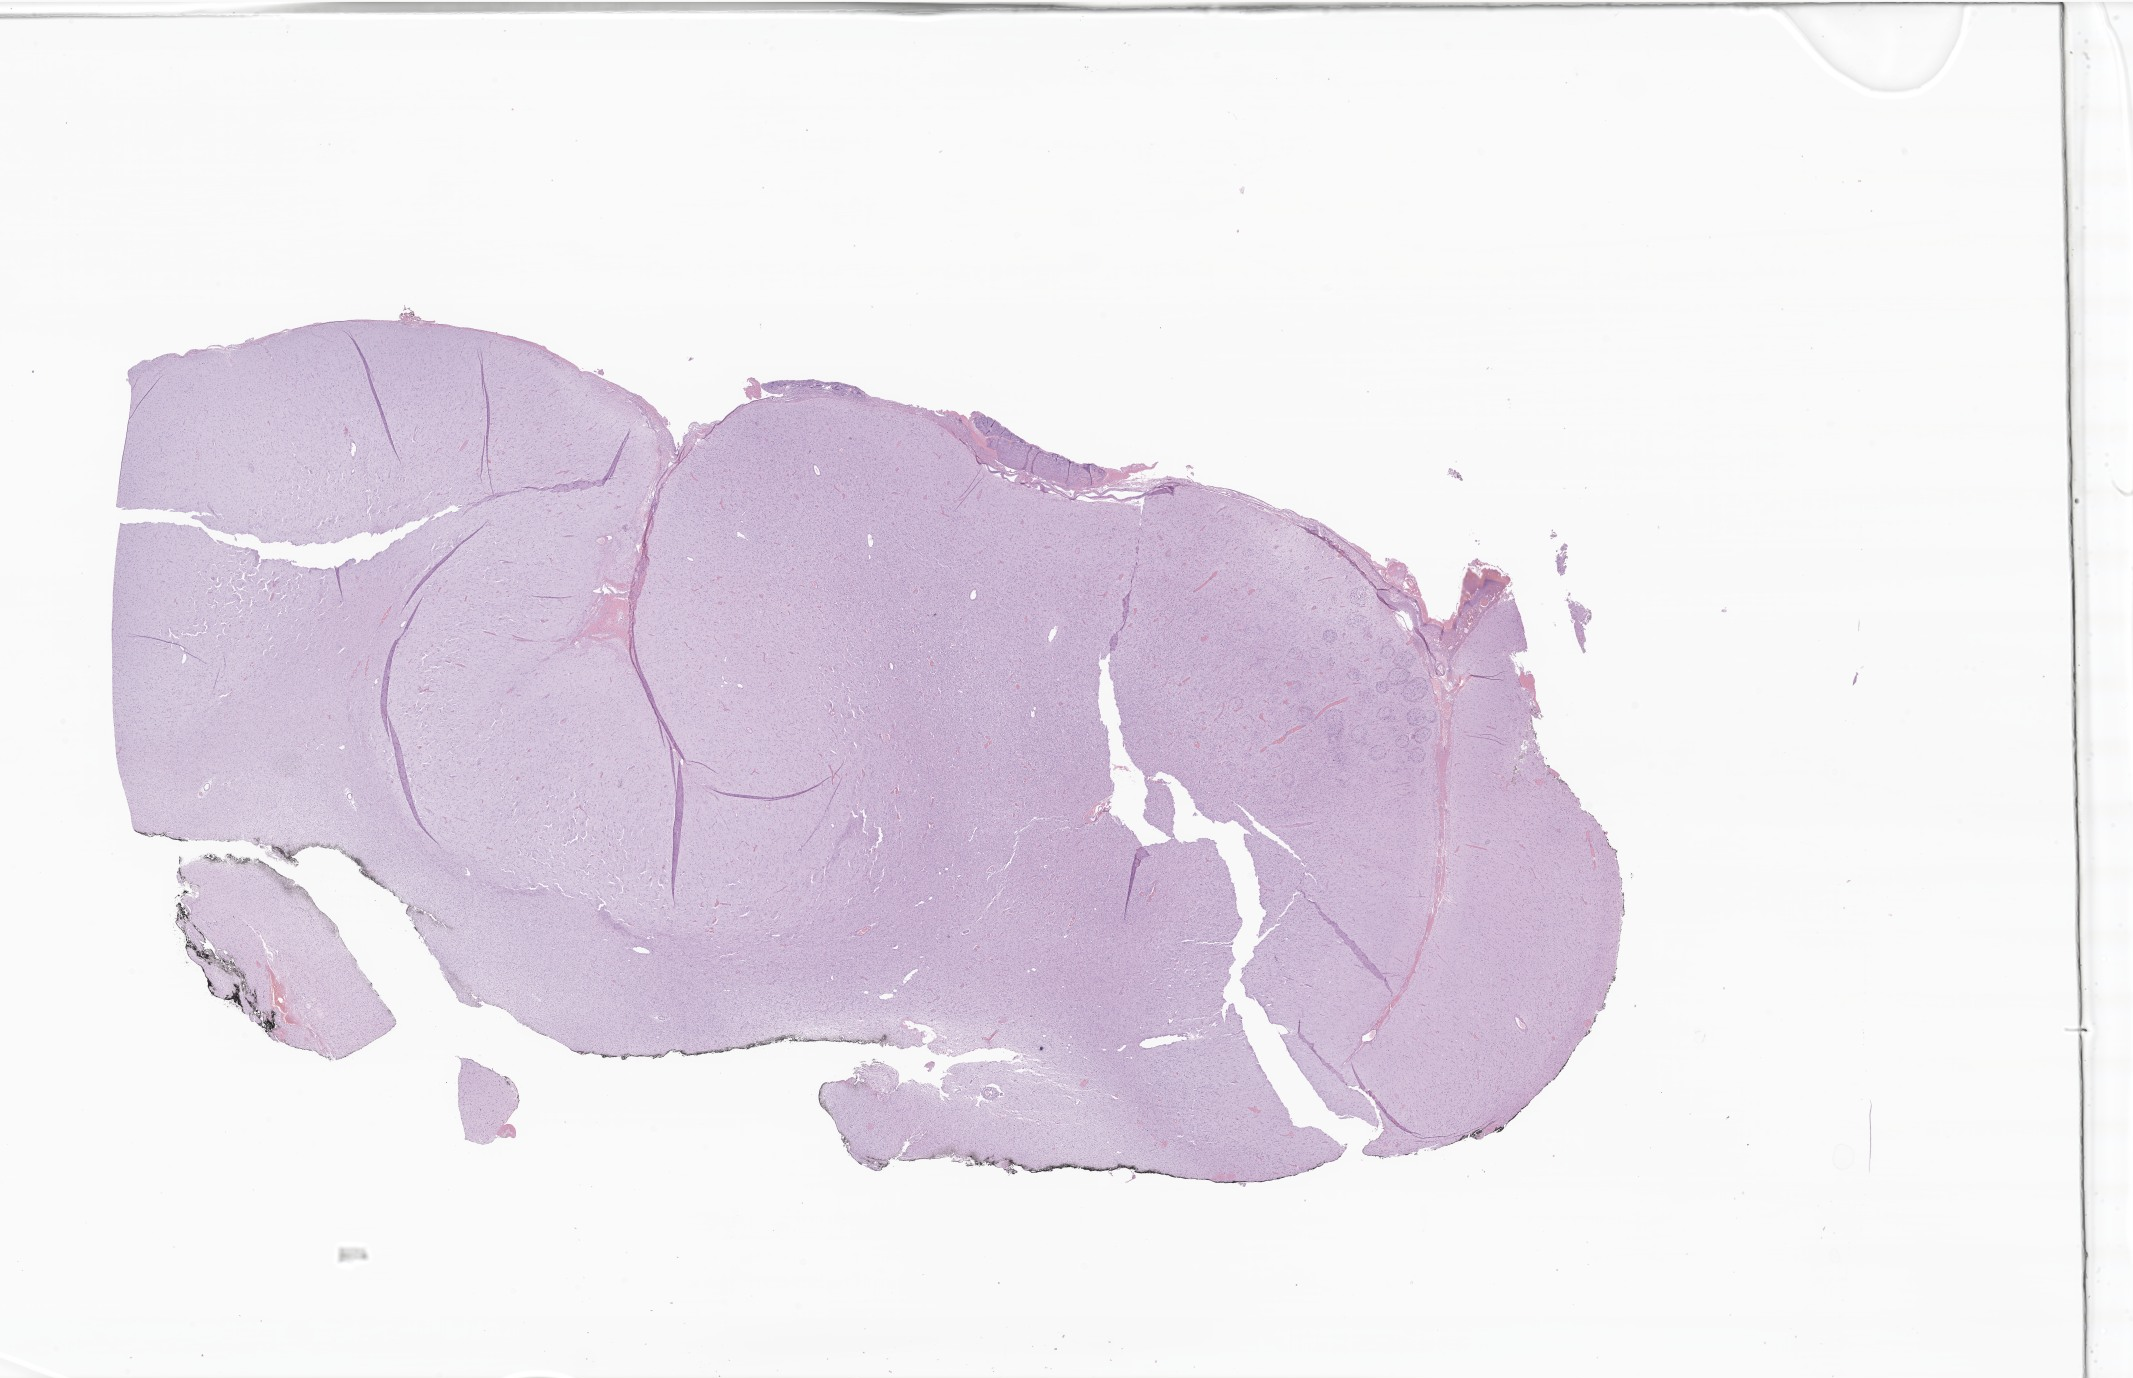
Whole-slide image, hematoxylin and eosin (H&E) stain of tumor tissue from the brain, whole scanned area (about 36.0 x 23.2 mm) shown as a low-resolution overview; formalin-fixed paraffin-embedded section. Patient male; age 111 months.
• recorded diagnosis: Glioma, malignant